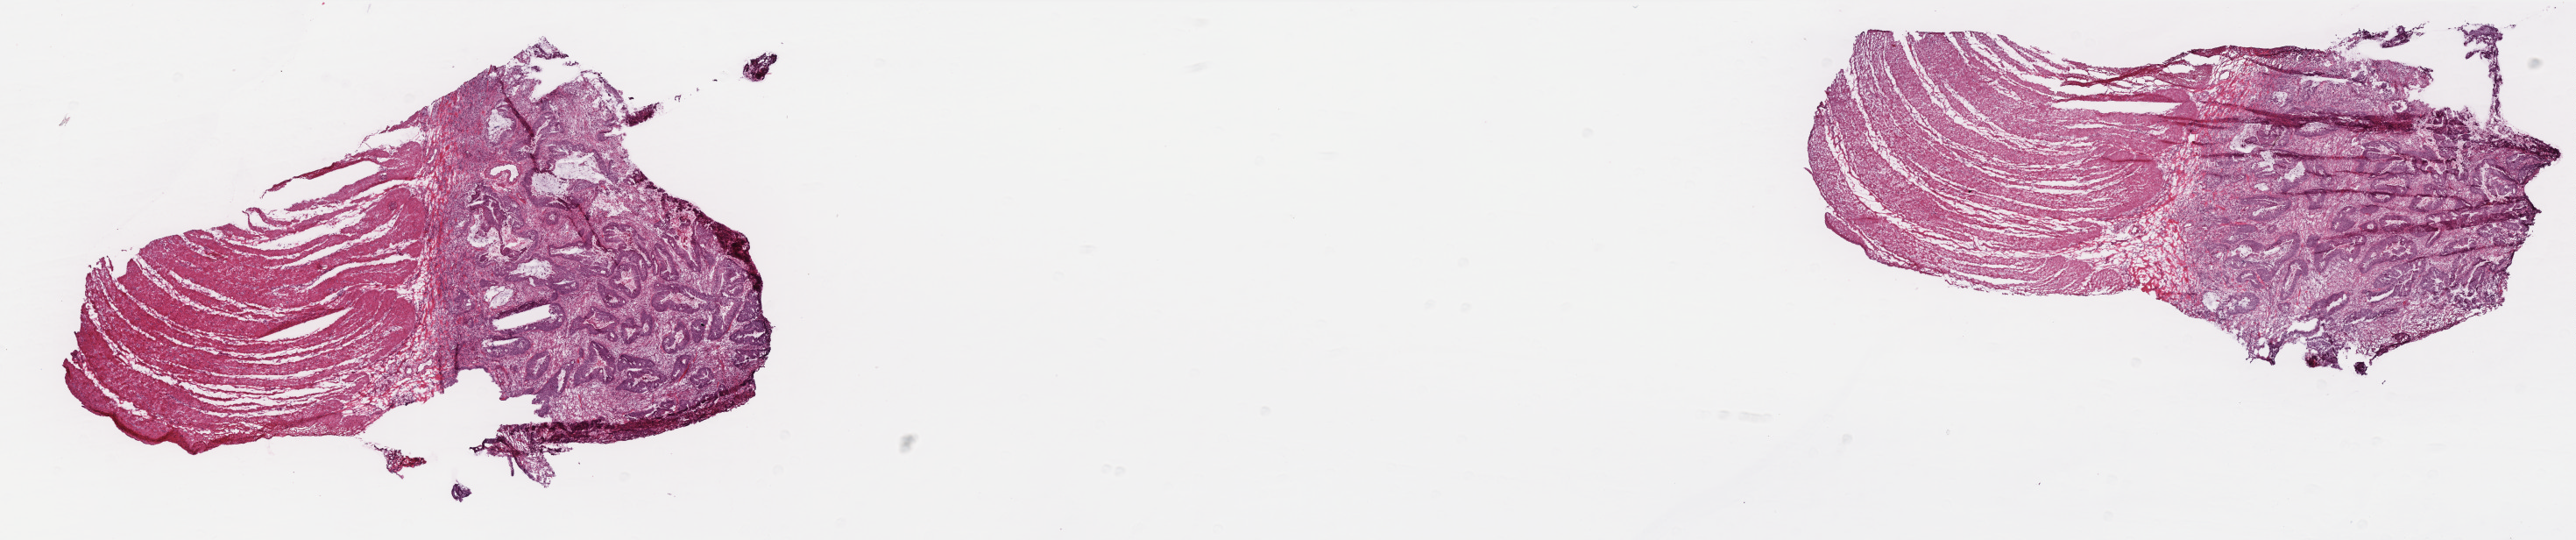
H&E-stained whole-slide image, a low-resolution overview of the entire scanned area, about 23.6 x 4.9 mm (from a 40x scan), frozen section, primary tumour sample from the colon. Male, age 79 years at initial diagnosis.
Histologic diagnosis: Adenocarcinoma, NOS (sigmoid colon).